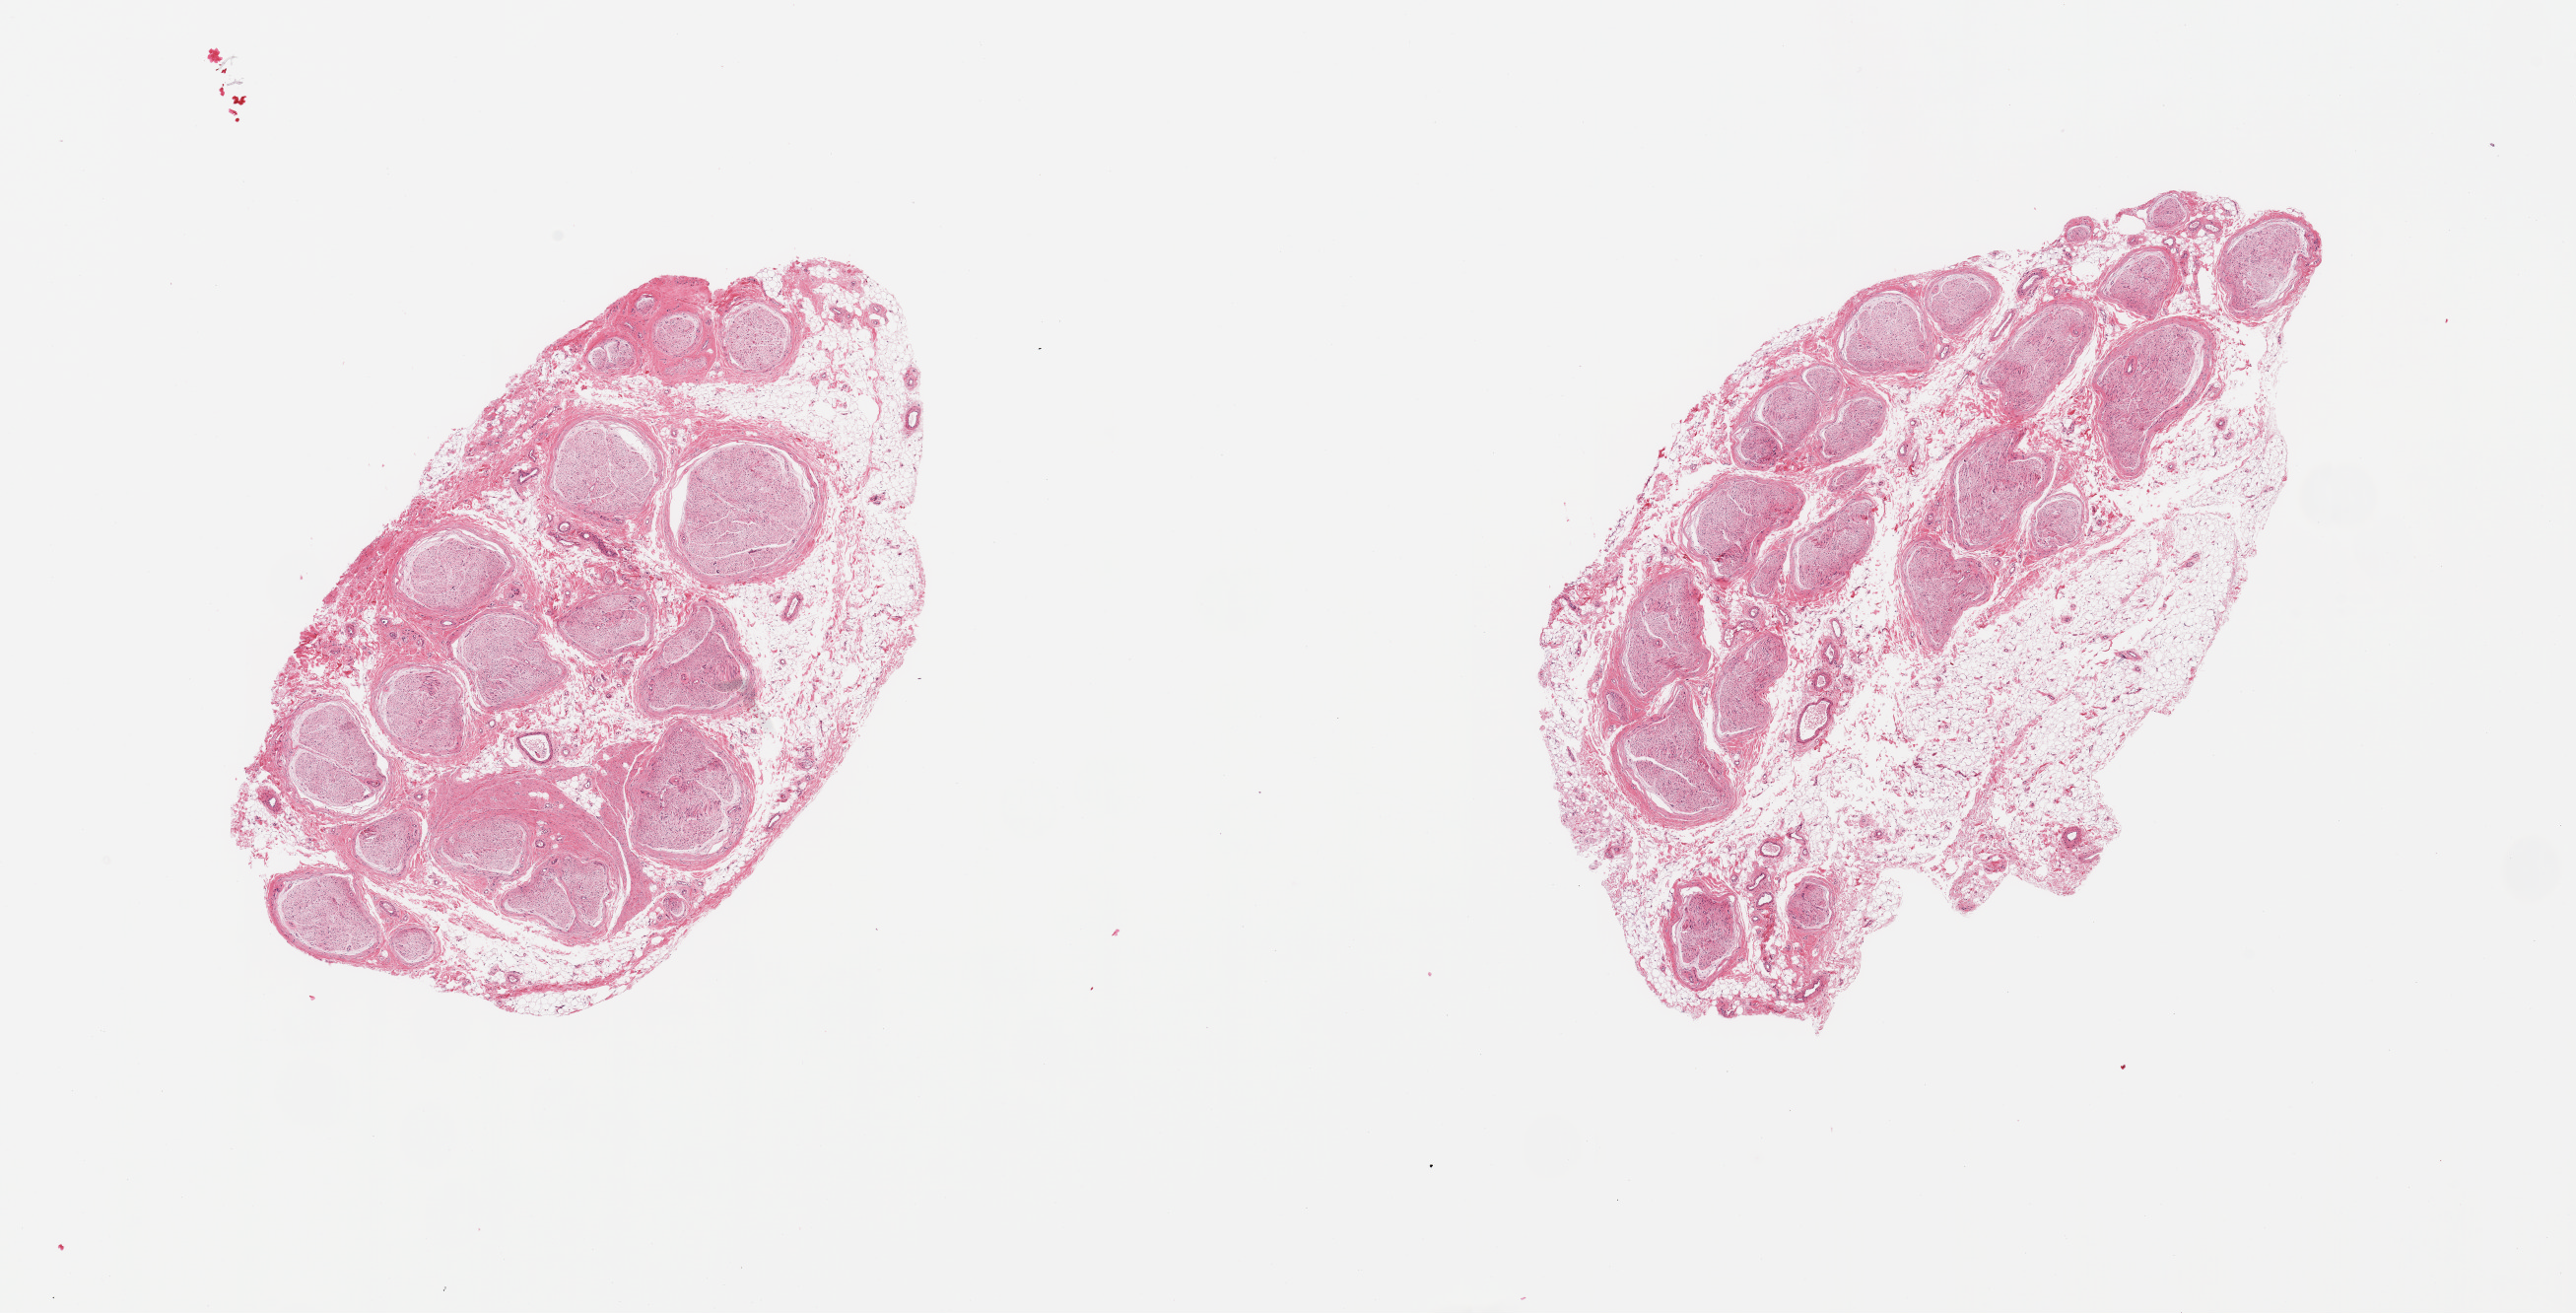
Digitized haematoxylin and eosin-stained section — low-resolution overview of the scanned area, about 20.7 x 10.5 mm, PAXgene-fixed, paraffin-embedded tissue, target tissue: tibial nerve, tissue donor sample. Donor: female.
Review note (as recorded): 2 pieces; 30 & 40% internal & external fat; small arteries have thick sclerotic walls.